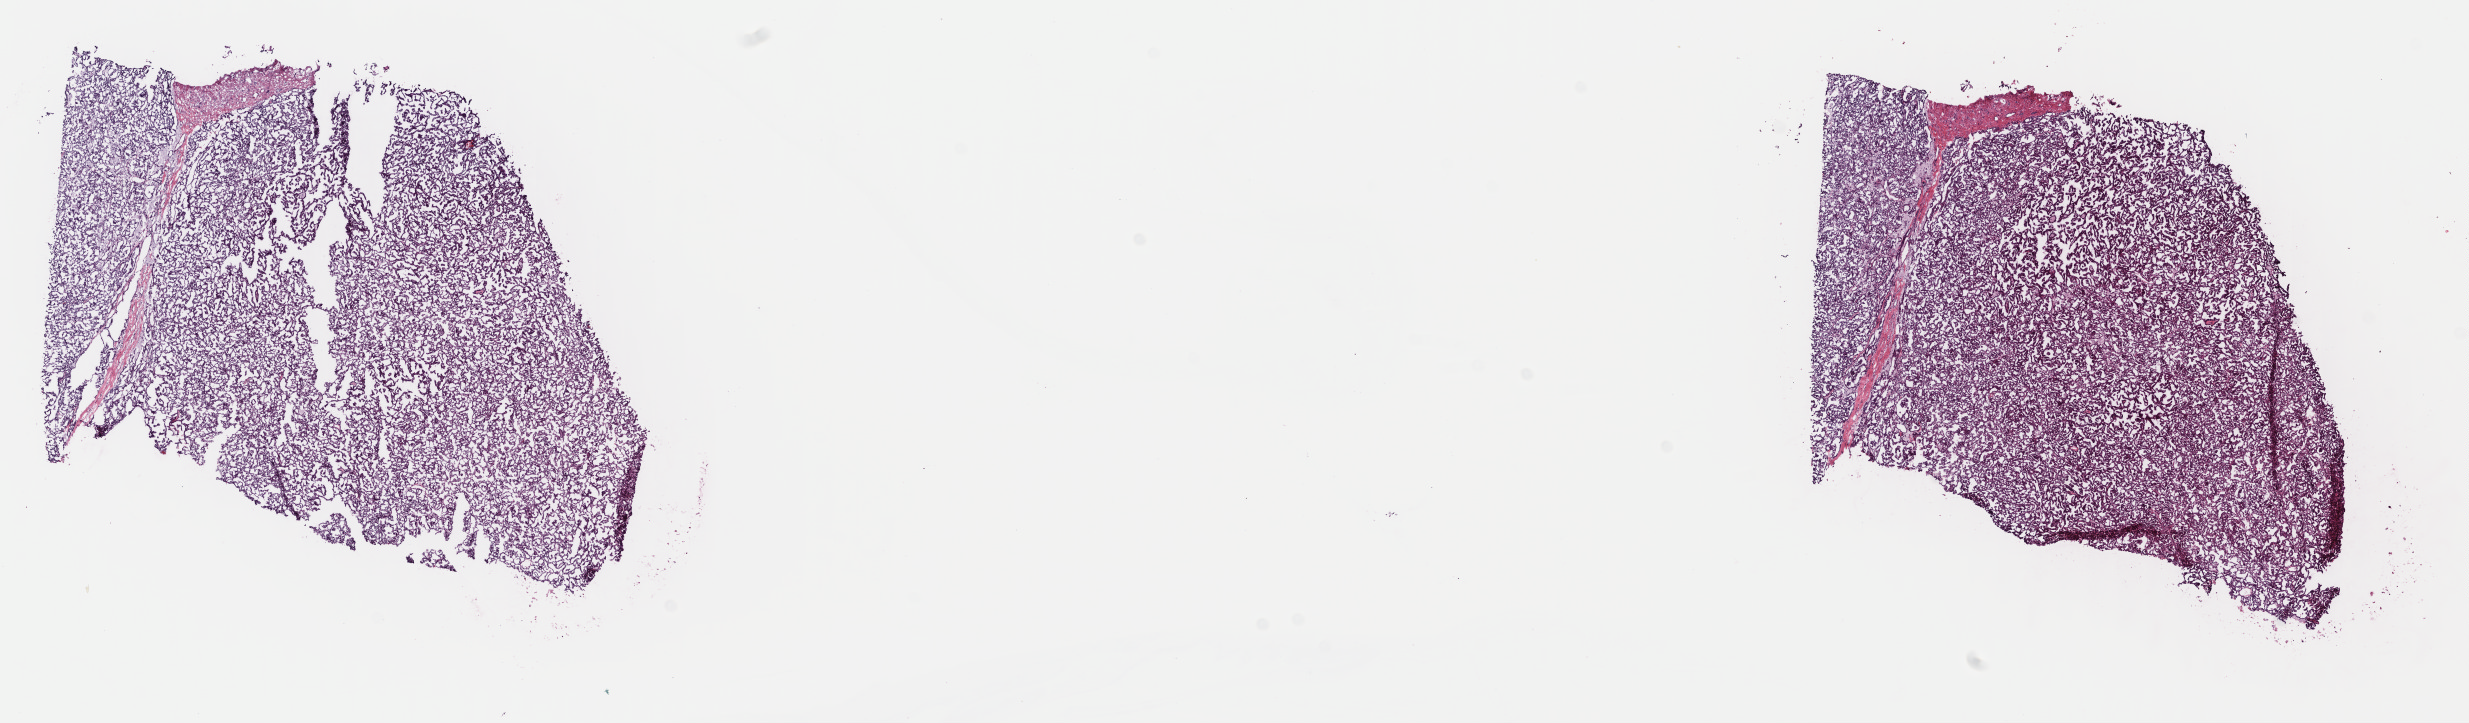
Digitized H&E tissue section (whole slide) — a low-resolution overview of the entire scanned area, about 19.4 x 5.7 mm (from a 40x scan), frozen section, sample: primary tumour, kidney. Male, age 51 years at initial diagnosis. Pathologist review of this section (percent, as recorded): tumour cells 80%, tumour nuclei 80%, normal cells 0%, stromal cells 20%, necrosis 0%. Infiltration values recorded for this section: lymphocyte infiltration 0%, monocyte infiltration 5%, neutrophil infiltration 0%.
• histologic diagnosis: Papillary adenocarcinoma, NOS
• TNM: T1a N0 M0
• lymph nodes positive (case pathology): 0 of 6 examined
• AJCC pathologic stage: I